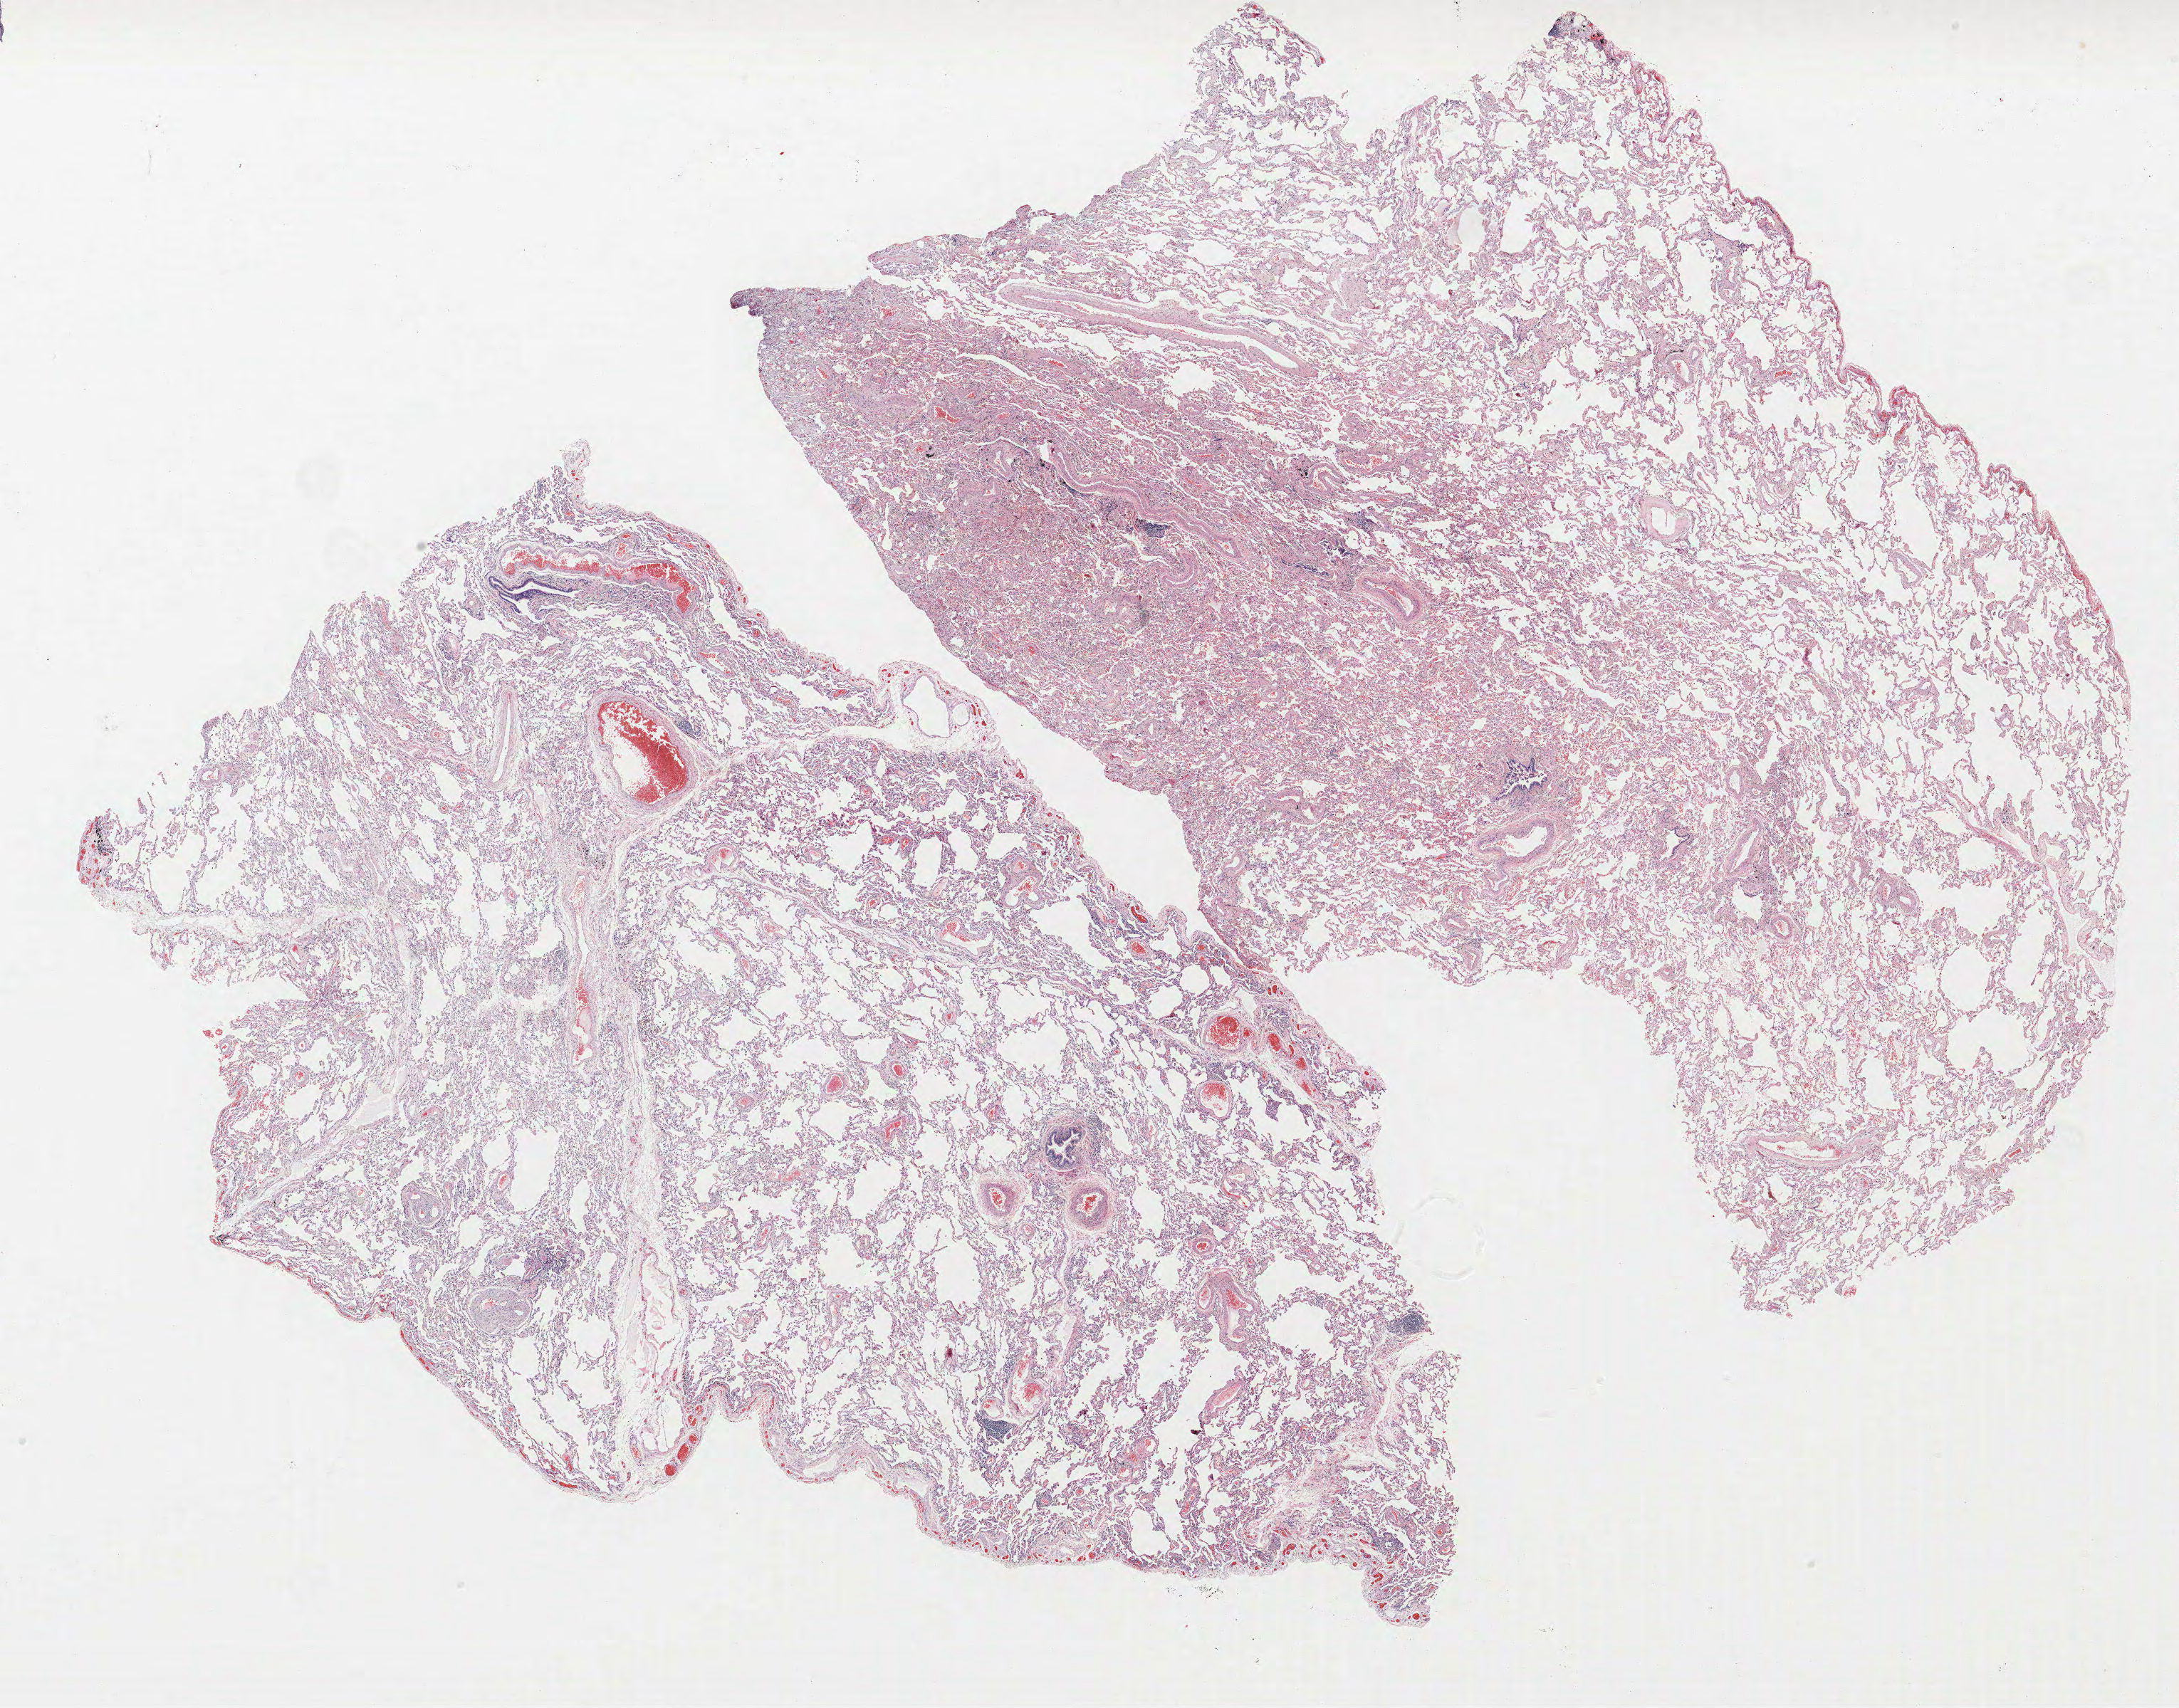
Whole-slide histology image, Hematoxylin and eosin (H&E) stained, whole scanned area (about 24.5 x 19.2 mm) shown as a low-resolution overview, formalin-fixed paraffin-embedded (FFPE) section, lung. Female patient, aged 71 at enrolment. Current smoker at enrolment. Grade: poorly differentiated (G3).
Primary tumour location (clinical record): right lower lobe. Participant's lung-cancer diagnosis: Squamous cell carcinoma, NOS (ICD-O-3 8070/3). Tumour size (pathology): 8 mm. ICD-O-3 topography: lower lobe of lung (C34.3). Stage (AJCC 6th edition): IA.